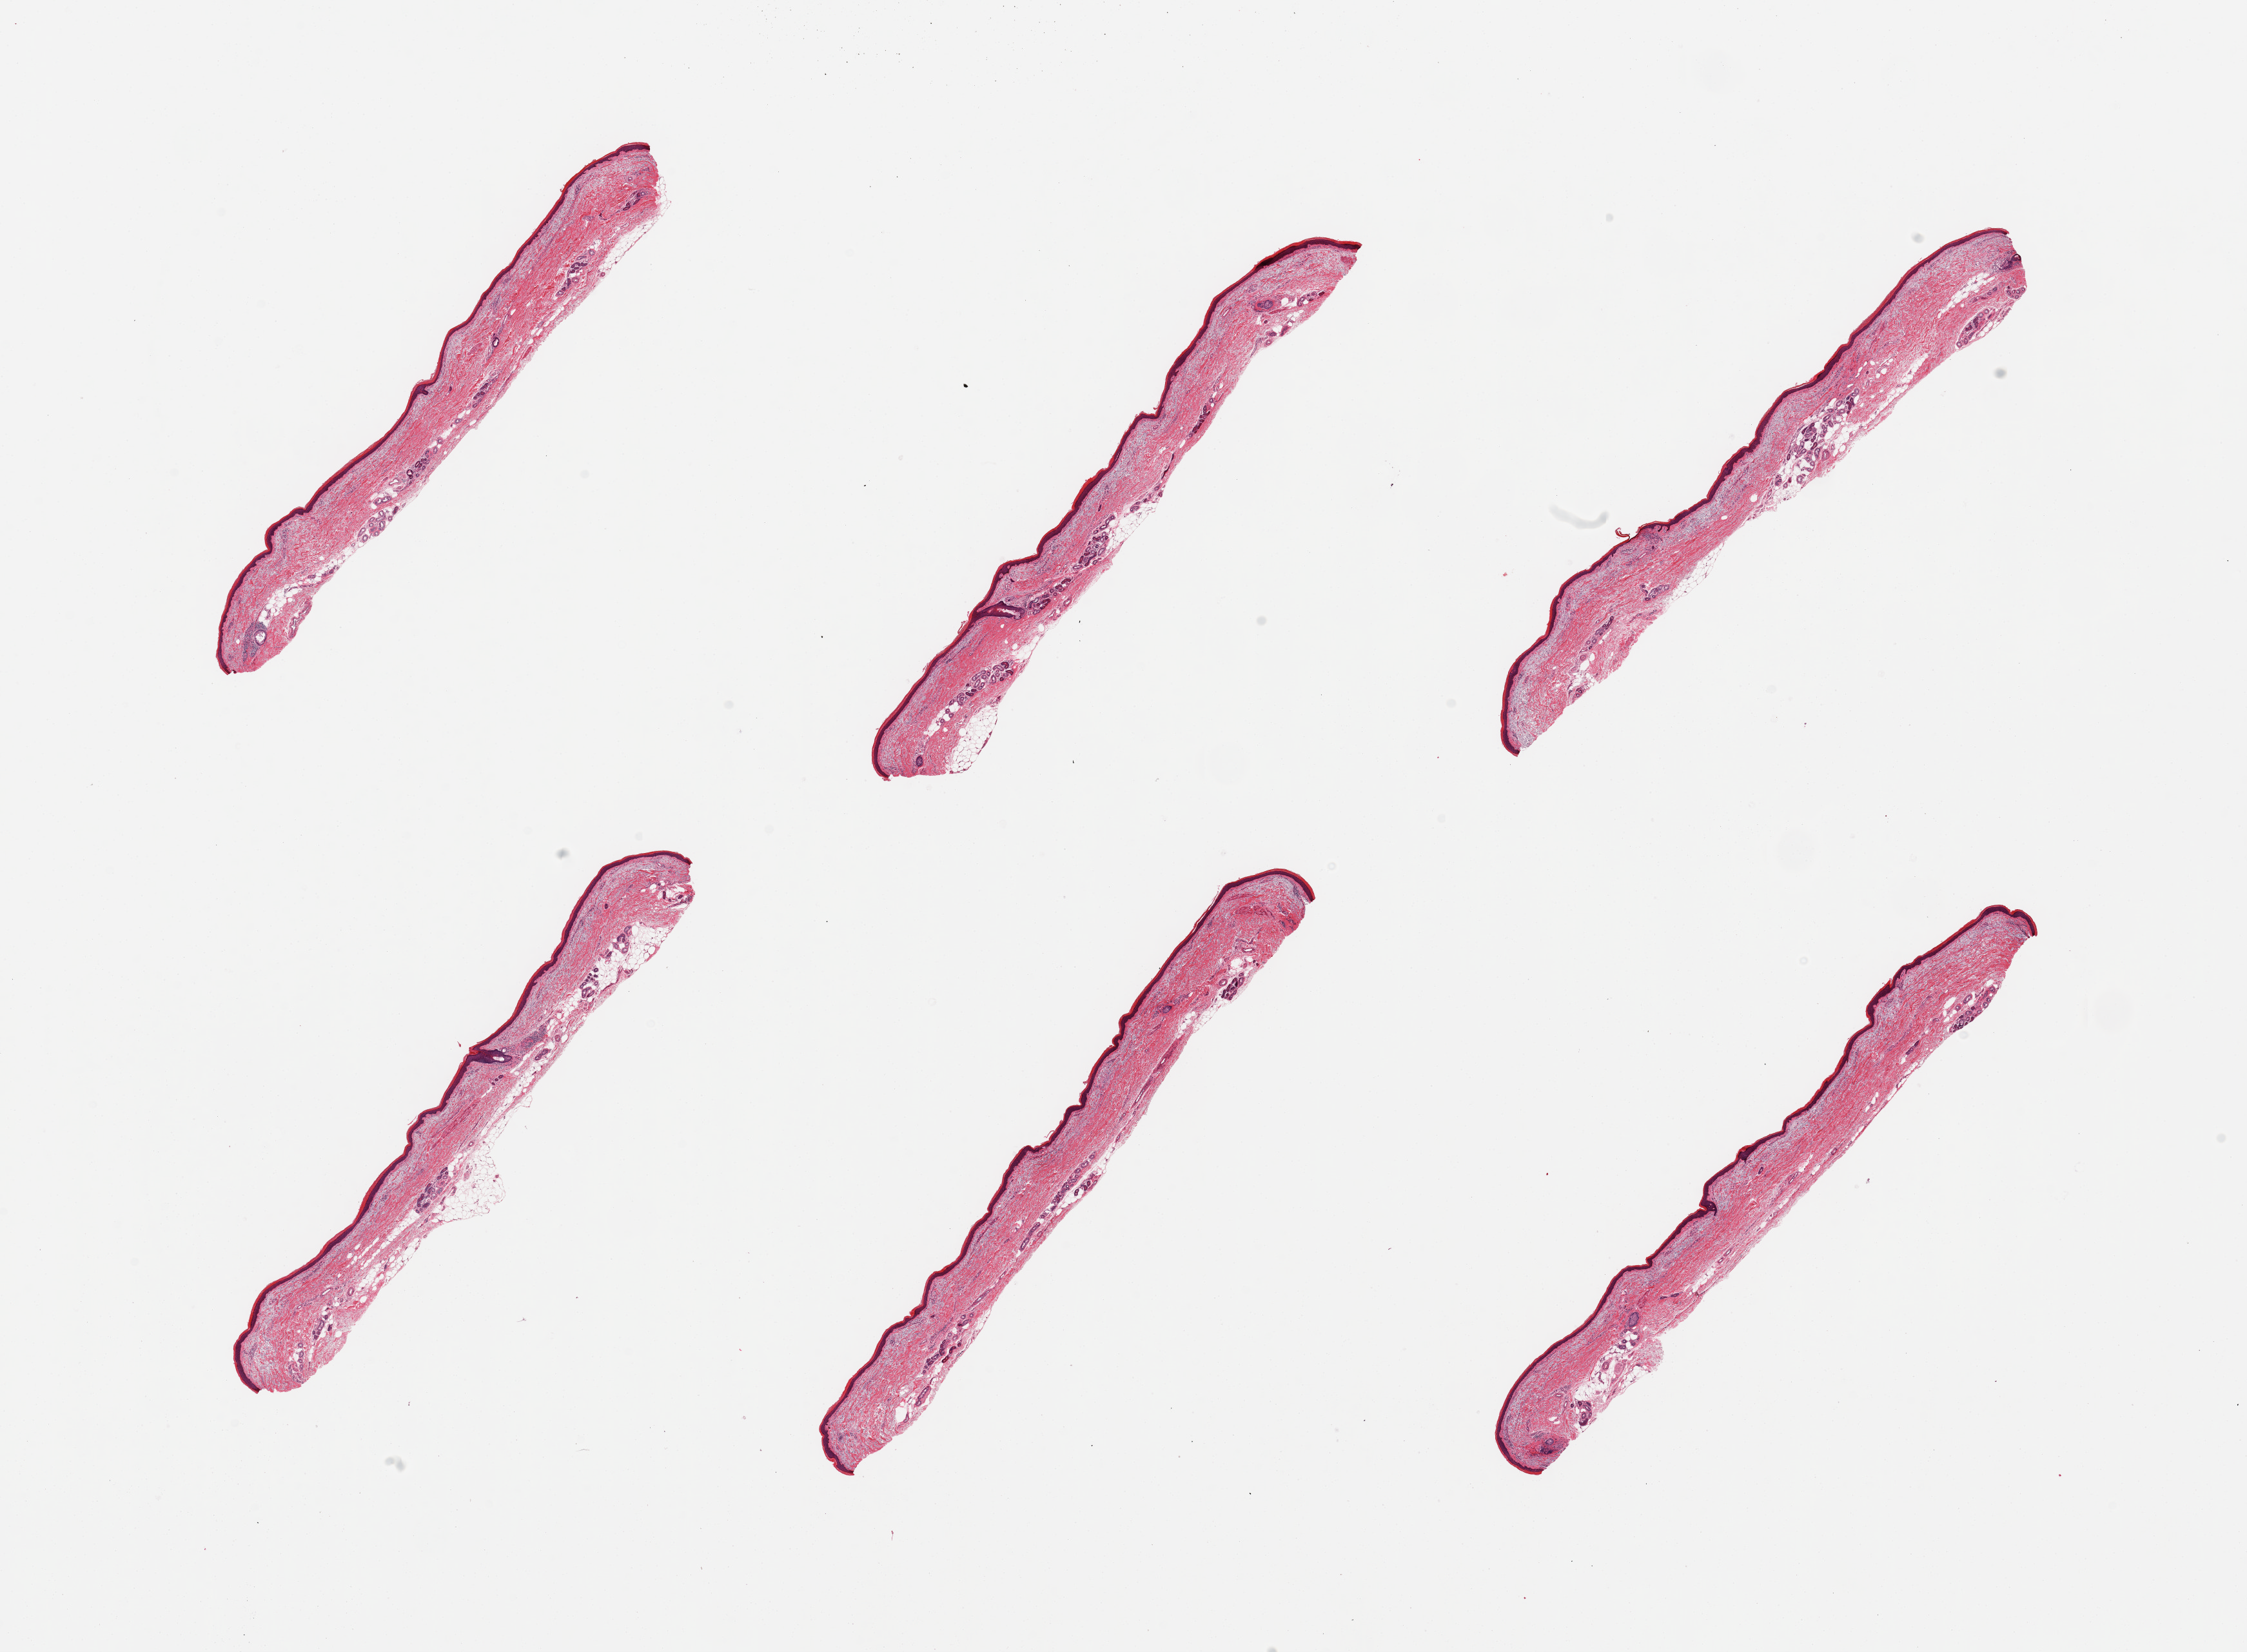
Whole-slide image, haematoxylin and eosin stain, brightfield — shown as a low-resolution overview of the whole scanned area (about 27.6 x 20.3 mm, acquisition: 20x scan), PAXgene-fixed paraffin-embedded (PFPE) section, target tissue: skin of lower leg, tissue donor sample.
Review note (as recorded): 6 pieces; solar elastosis, epidermis measures 41 um thick.